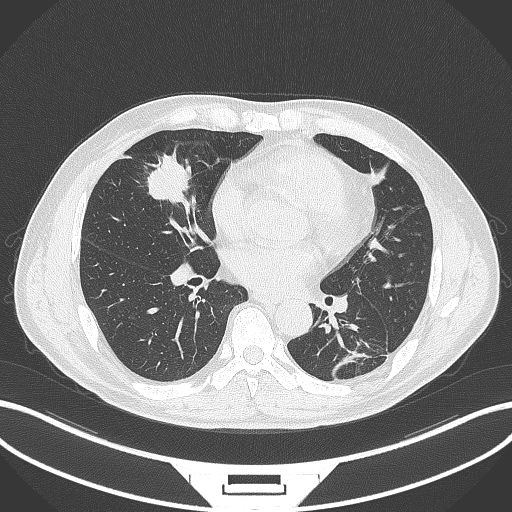
Chest CT, one axial slice; position 134 of 399 along the scan axis; reconstruction kernel B70f; 120 kVp; lung window (W 1500 / L -600 HU); 1 mm slice thickness; 512 × 512 image matrix, field of view 400 × 400 mm. Male patient, age 59 years. From the clinical record (not read from this slice): clinical TNM (as recorded): T2a N1 M0.
Structures marked on this image (rectangle marked by the reading radiologist):
- lung tumour (recorded histology: adenocarcinoma): bounding box <144,147,197,203> (left, top, right, bottom; pixels)